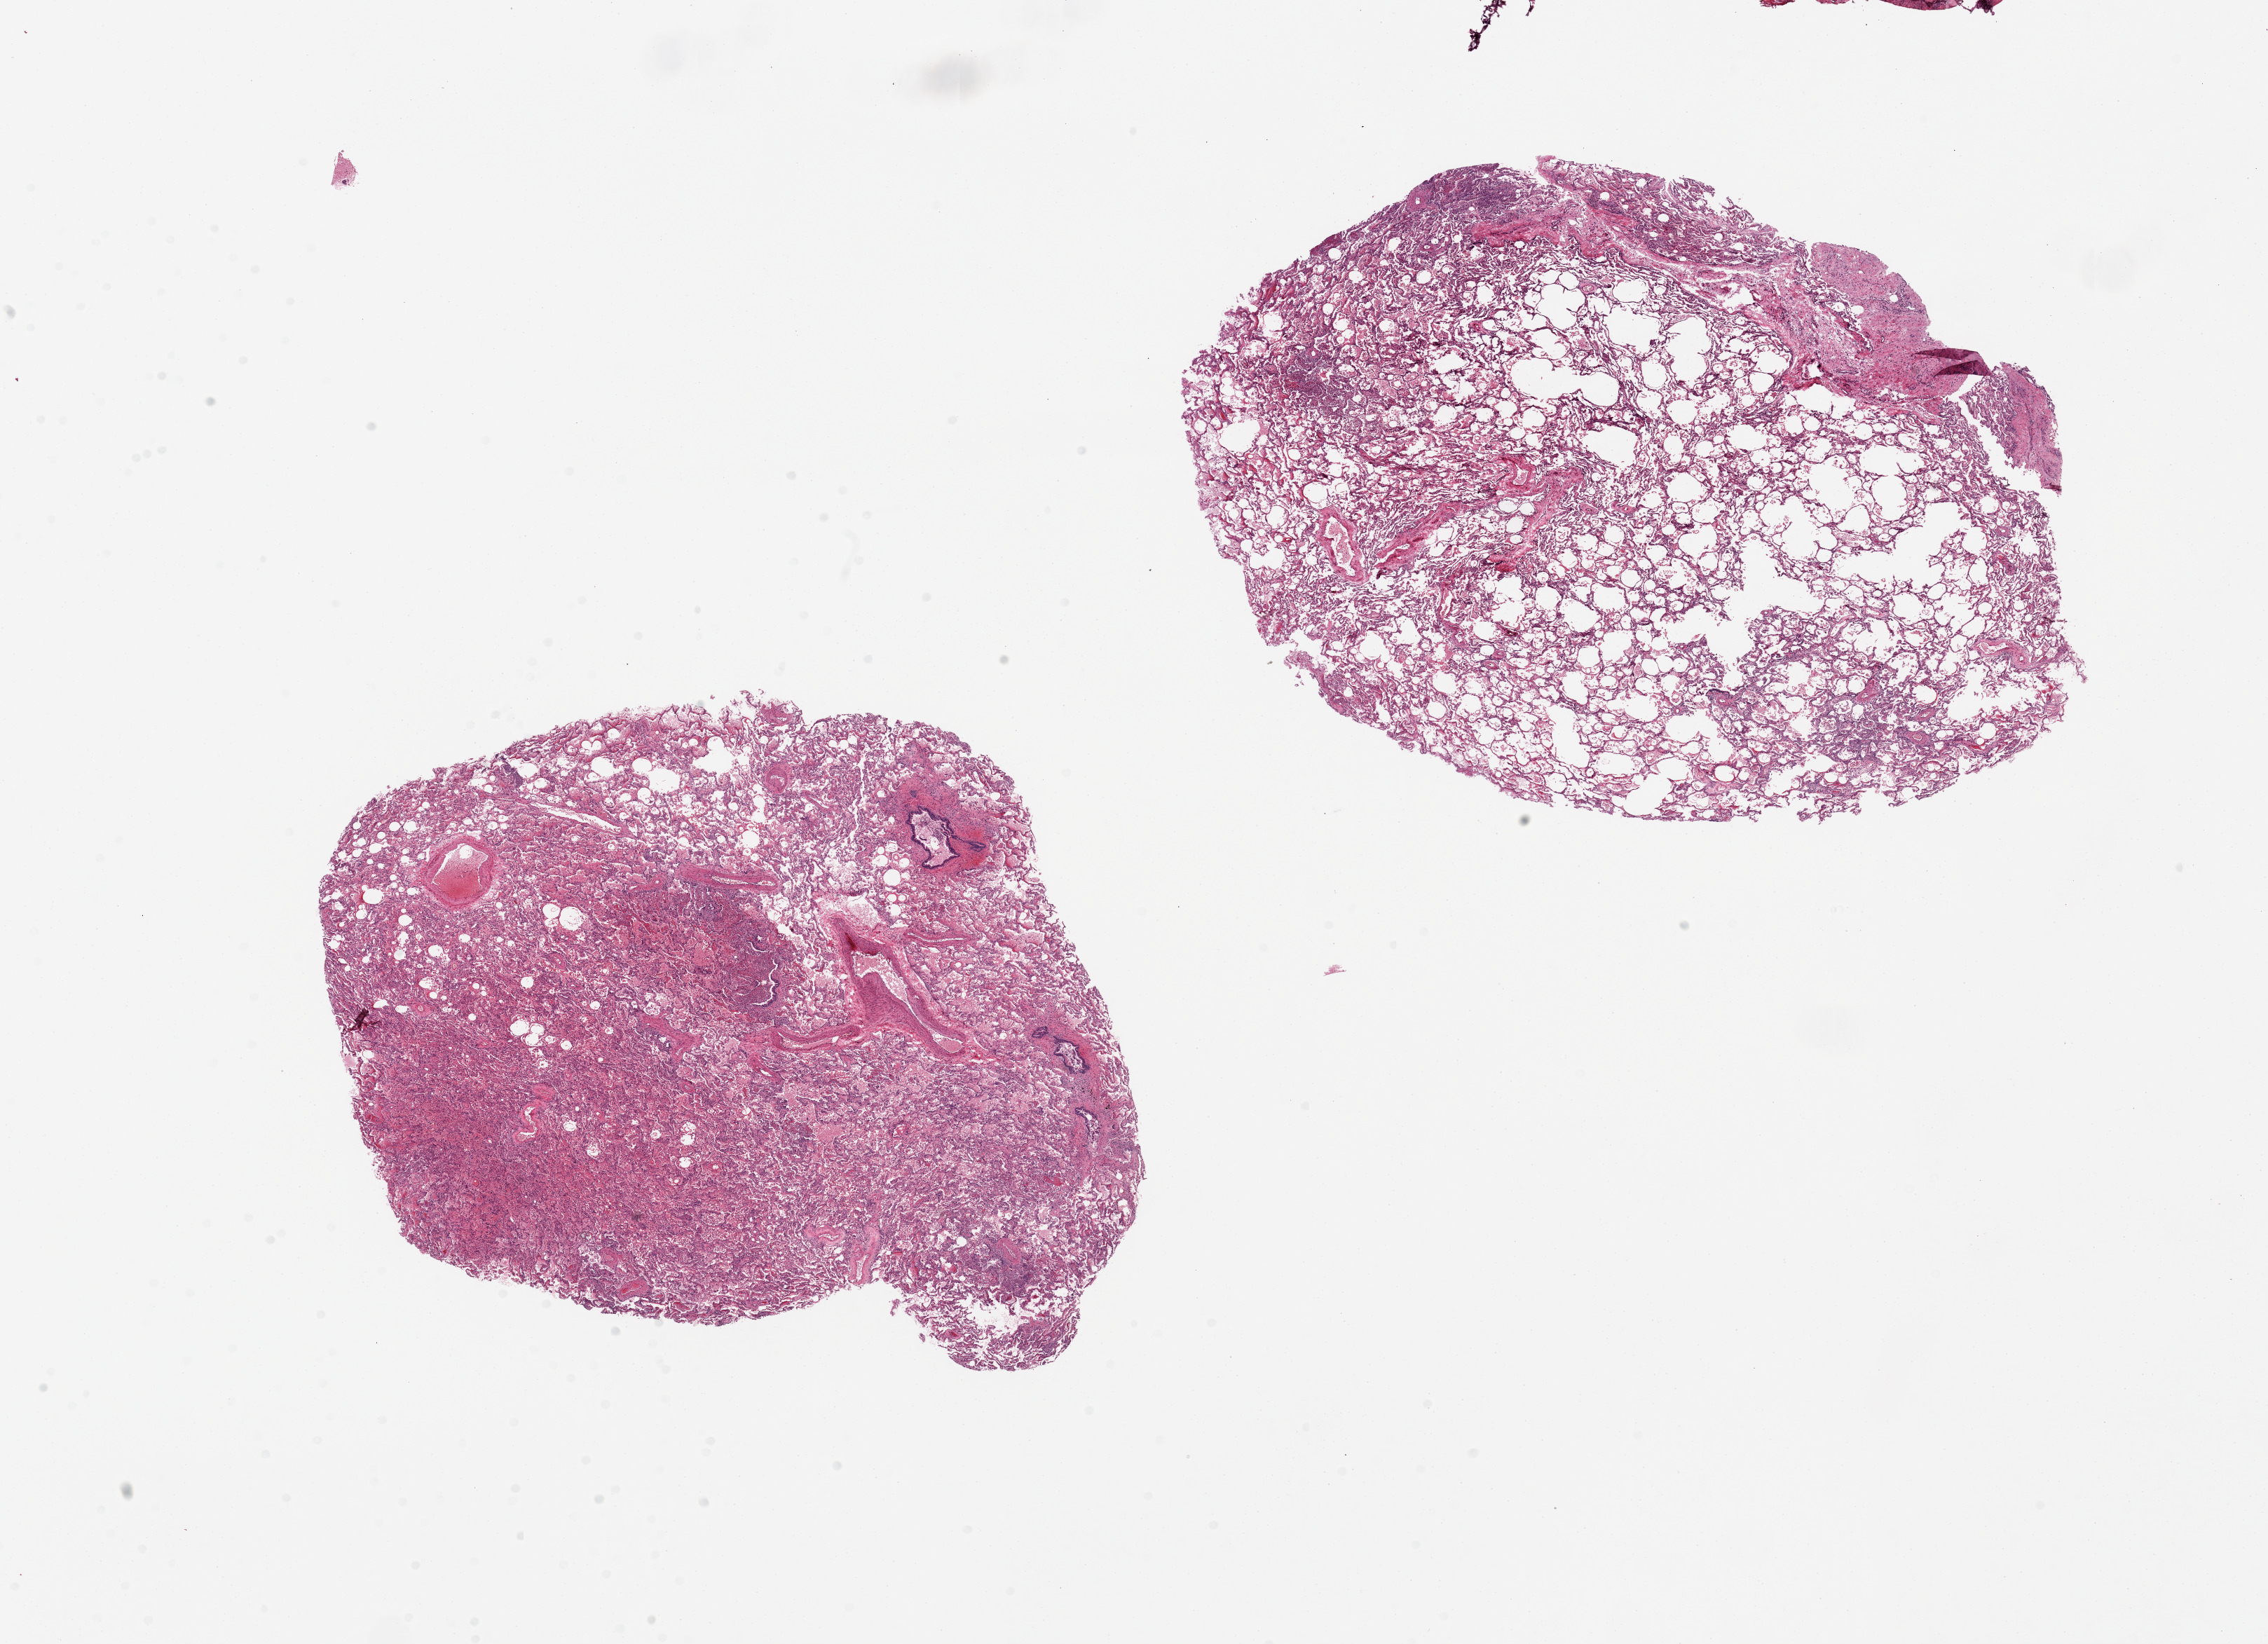
Haematoxylin and eosin whole-slide image — shown as a low-resolution overview of the whole scanned area (about 25.6 x 18.6 mm, acquisition: 20x scan). PAXgene-fixed paraffin-embedded (PFPE) section. Target tissue: lung. Donor tissue sample. Donor sex: male.
Pathologist's review note for this sample: 2 pieces, 9x8 & 10x8mm; diffuse, acute broncho pneumonia, densest areas.